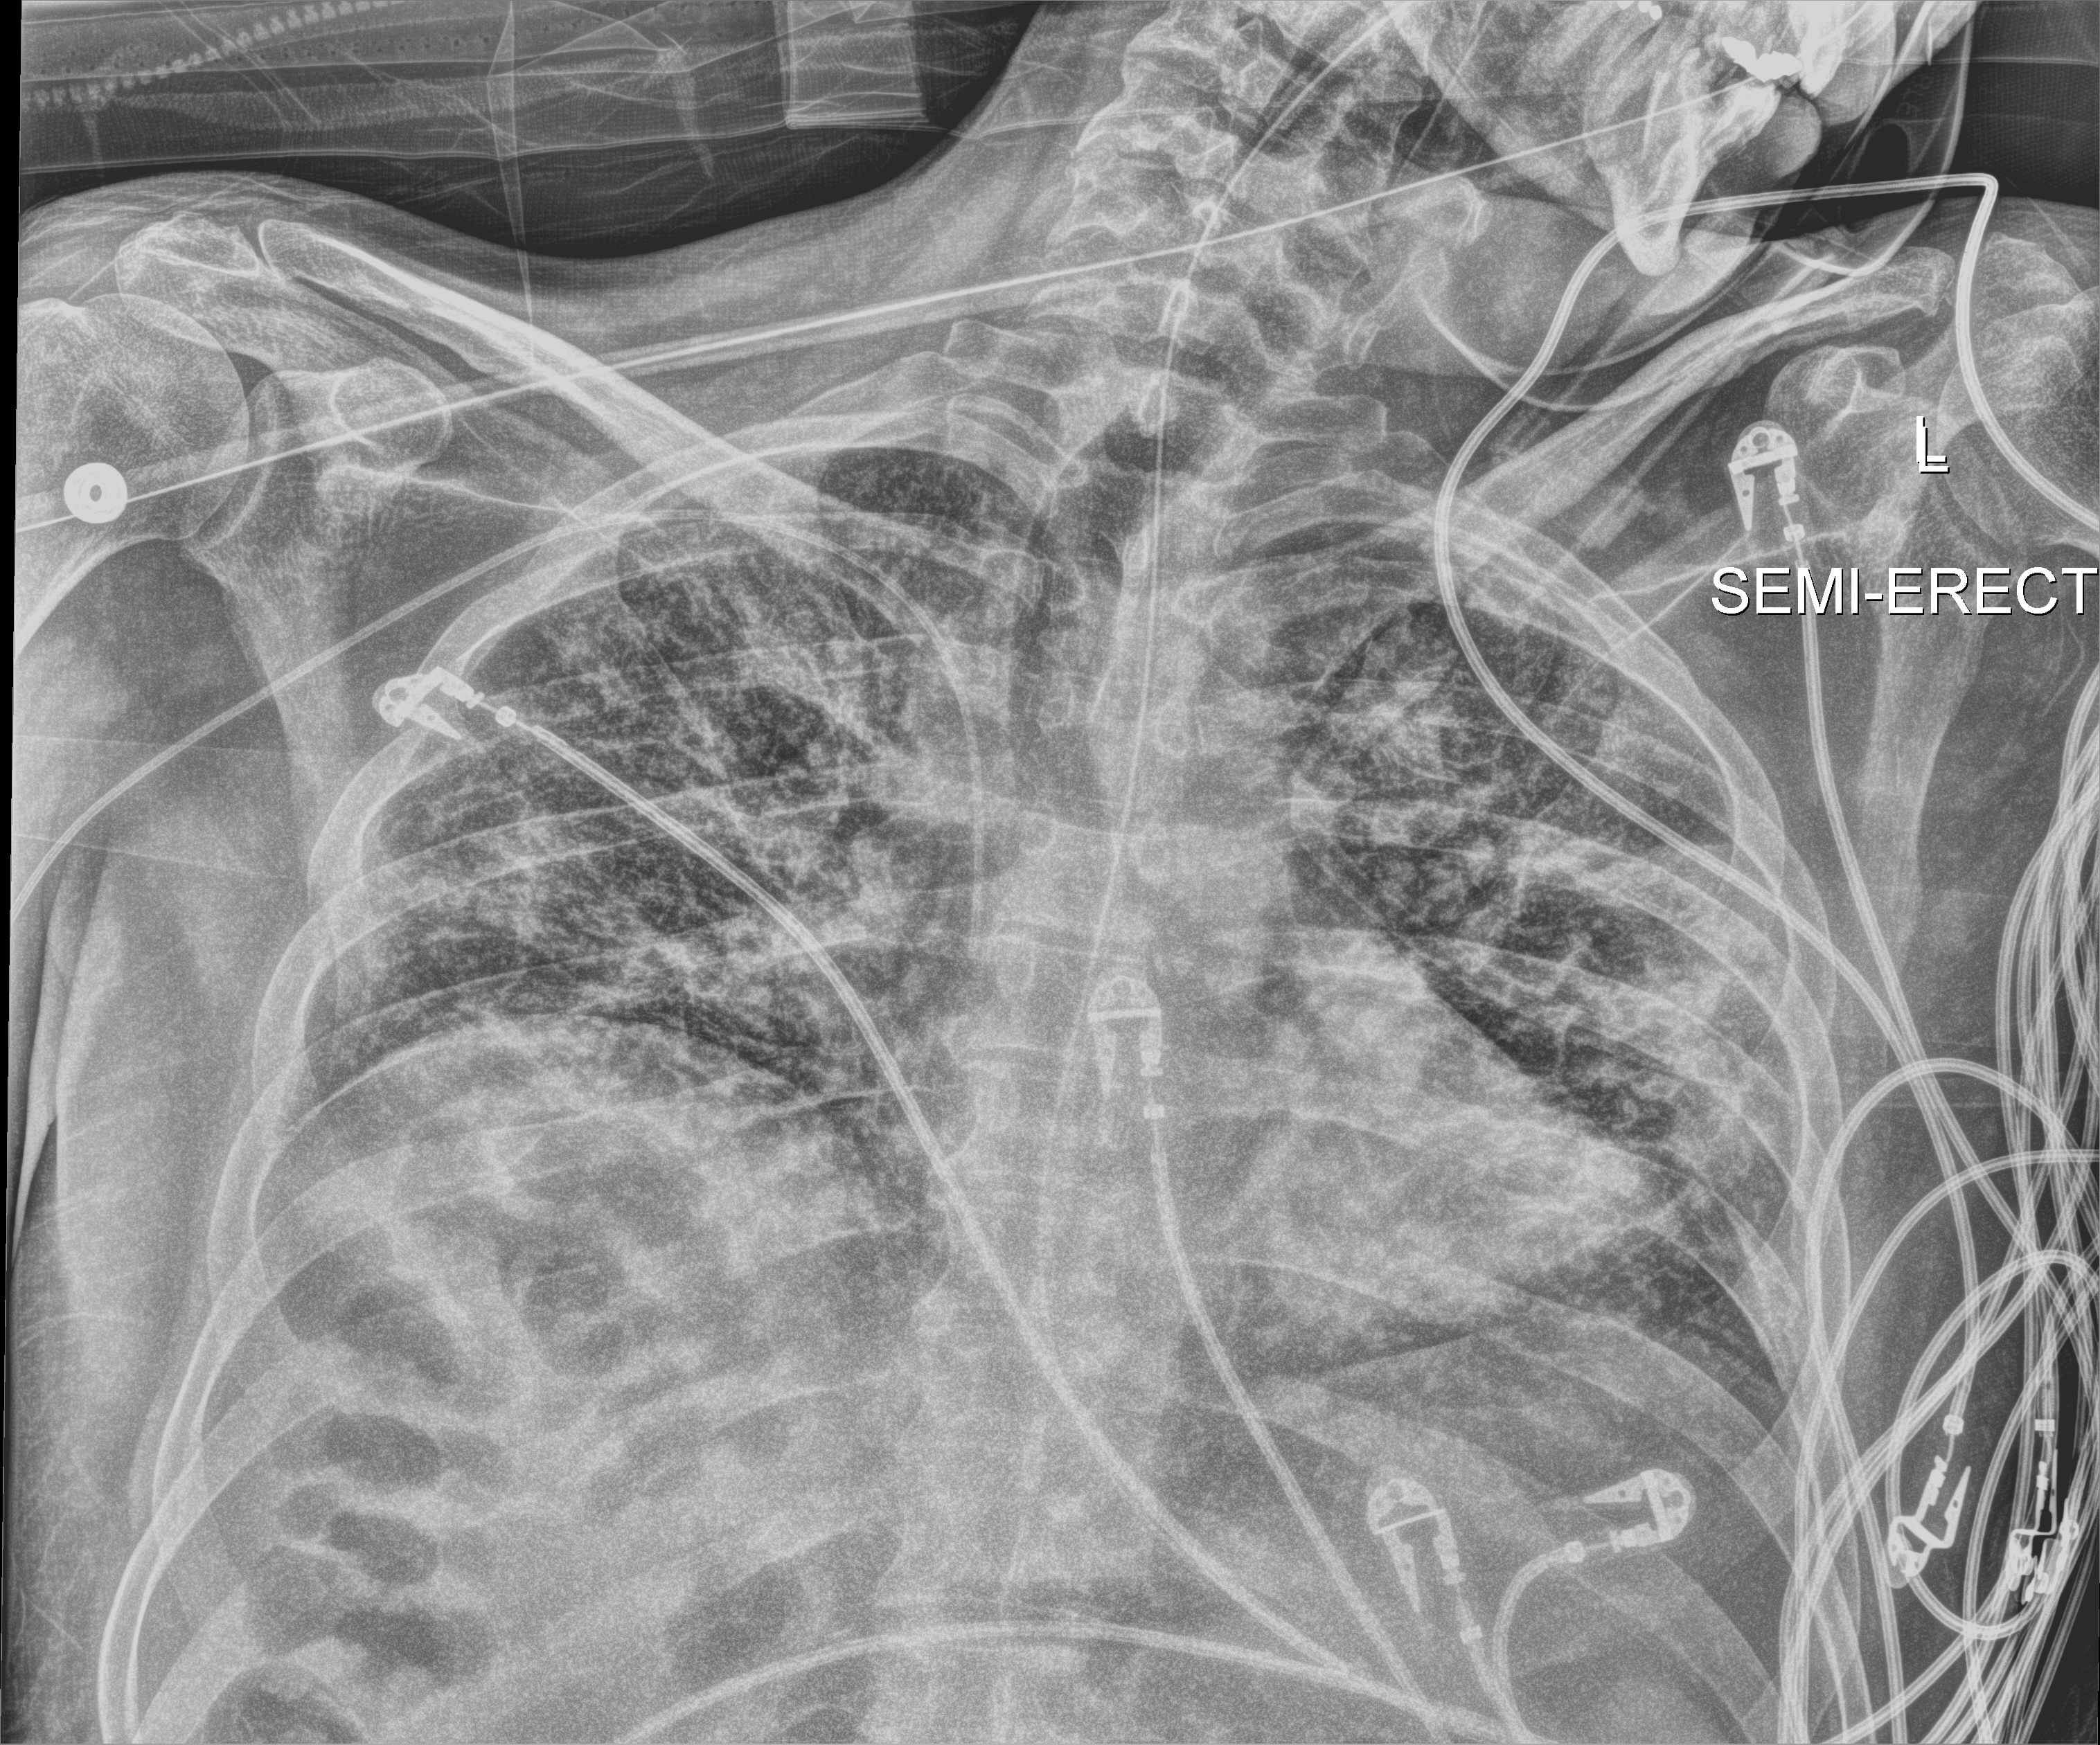
Chest X-ray (portable); anteroposterior (AP) projection. Male patient hospitalised with COVID-19, age 18–59 years.
Hospital-stay facts (about this admission, not read from this image; timing relative to this image not recorded): length of hospital stay: 48 days; admitted to intensive care during this hospital stay: yes.